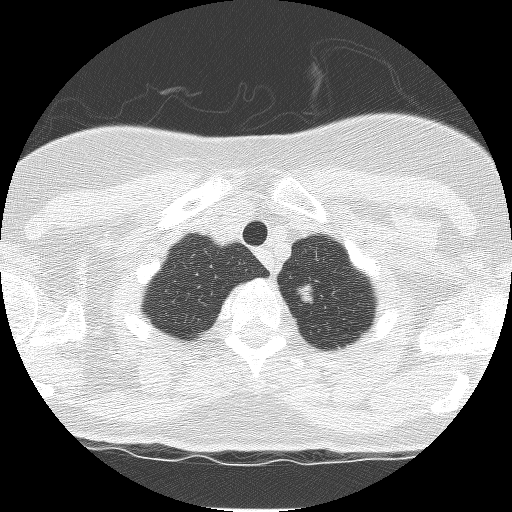
Low-dose screening chest CT, axial slice. Third annual screen. Lung window (W 1500 / L -600 HU). 2.5 mm slice thickness. Lung (sharp) reconstruction kernel (BONE). 120 kVp. Slice 10 of 120 in the series. Female, age 59 years at enrolment. Former smoker at enrolment.
- Expert-annotated lung lesion, bounding box (x1, y1, x2, y2) in pixels: (278, 270, 331, 319).
- The screening reader recorded 3 non-calcified nodules or masses ≥4 mm on this exam (right upper lobe, left upper lobe, right upper lobe); which of them this box marks is not recorded.
- Official screen result: positive, other.
- Later outcome: lung cancer diagnosed 42 days after this screen — bronchiolo-alveolar adenocarcinoma, NOS, left upper lobe, well differentiated (G1), stage IA (AJCC 6th edition), 10 mm at pathology.